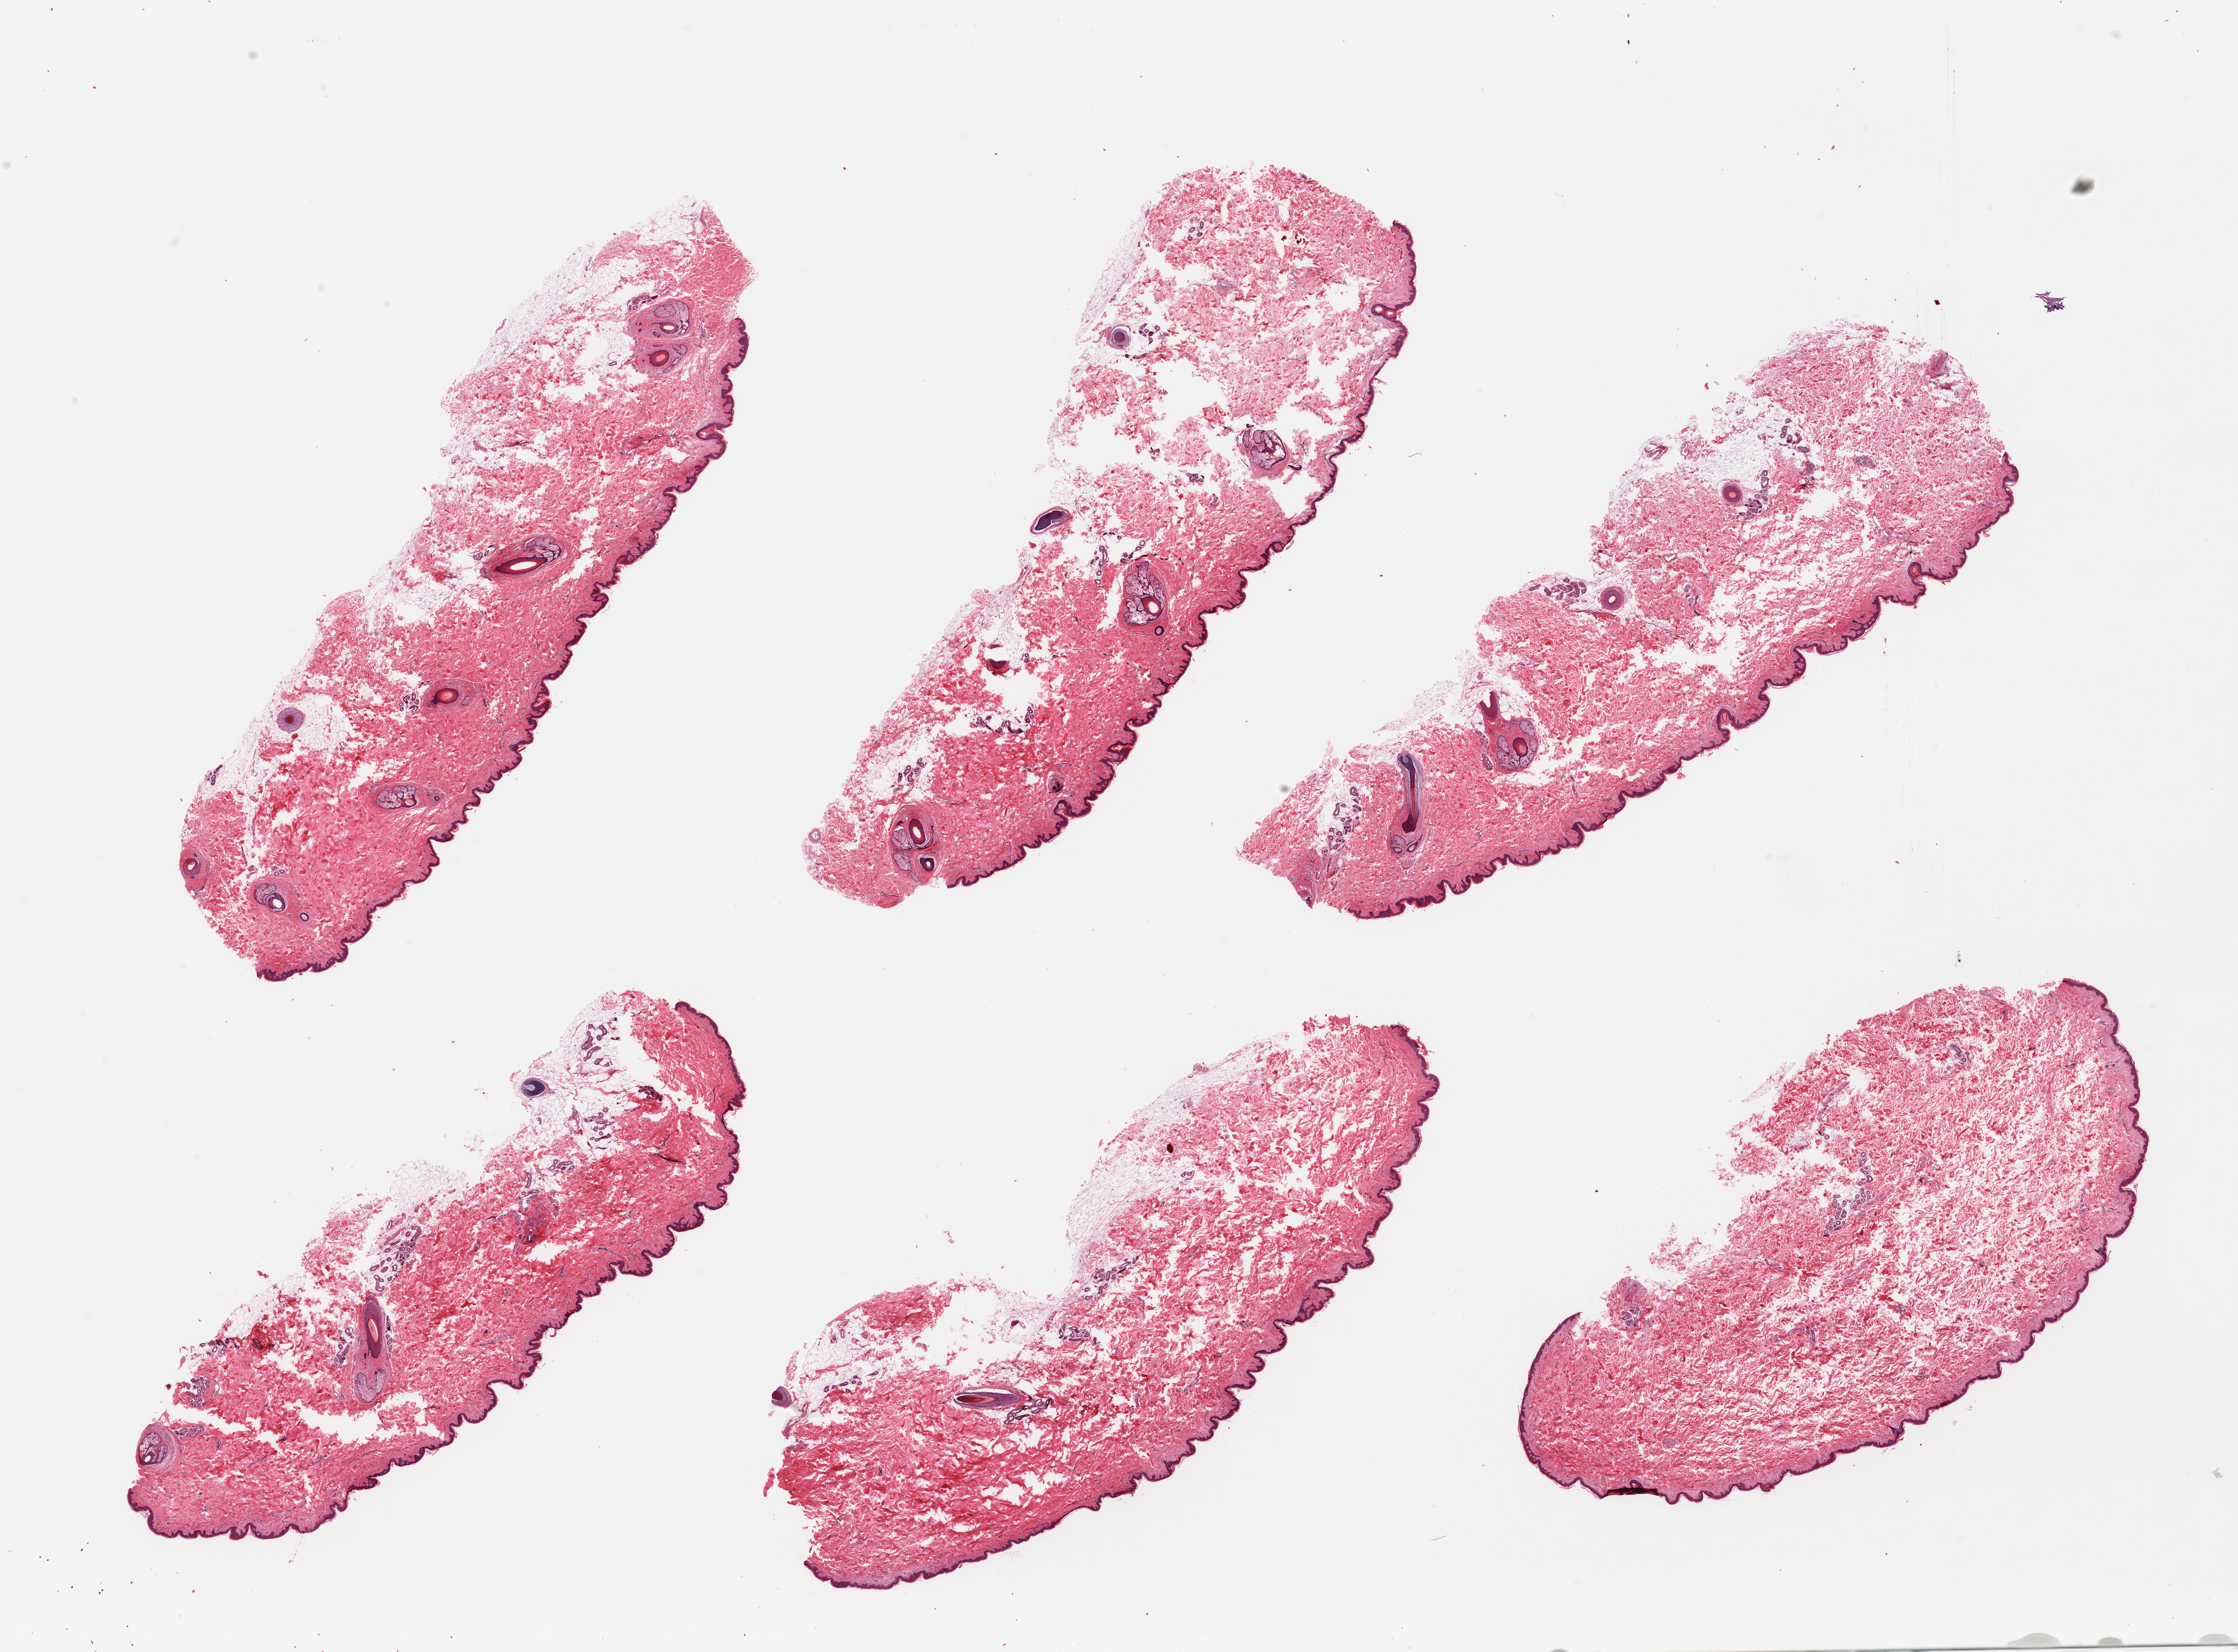
Digitized haematoxylin and eosin-stained section, brightfield — a low-resolution overview of the entire scanned area, about 30.5 x 22.5 mm (from a 20x scan); PAXgene-fixed paraffin-embedded (PFPE) section; sampled site (target tissue): skin of suprapubic region; tissue donor sample. Donor sex: male.
Pathologist's review note for this sample: 6 pieces; hair-bearing skin, includes up to ~10% fat.